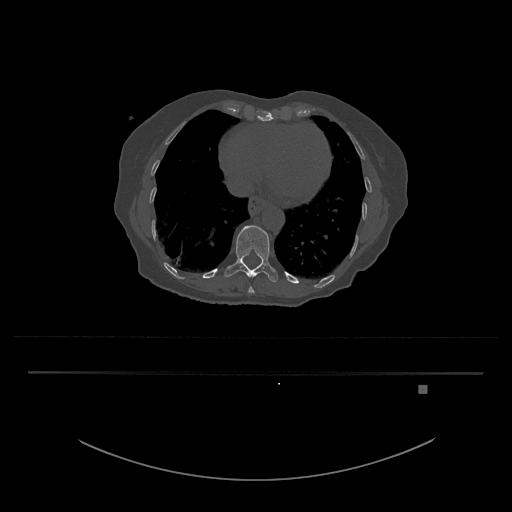
CT including the spine, one axial slice. Position 672 of 797 along the scan axis. 120 kVp. Bone window (W 1800 / L 400 HU). 512 × 512 image matrix. Patient: female, 57 years. From the clinical record (not read from this slice): primary cancer: cervical.
Structures marked on this image (semi-automatically segmented with operator editing):
- T10 vertebra: bounding box (x1, y1, x2, y2) in pixels: (248, 287, 255, 294)
- T11 vertebra: (224, 225, 278, 282)